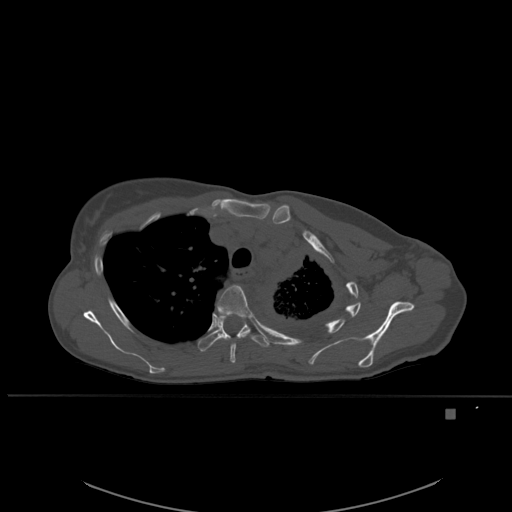
CT including the spine, one axial slice. Slice 406 of 537 in the series (ordered by position). Bone window (W 1800 / L 400 HU). 1.5 mm slice thickness. 512 × 512 image matrix. Female patient, age 45 years. From the clinical record (not read from this slice): primary cancer: lung.
Structures marked on this image (semi-automatic segmentation, software-assisted and operator-edited):
- T4 vertebra: bounding box [x1, y1, x2, y2] px = [217, 285, 252, 363]
- T5 vertebra: [198, 311, 270, 352]